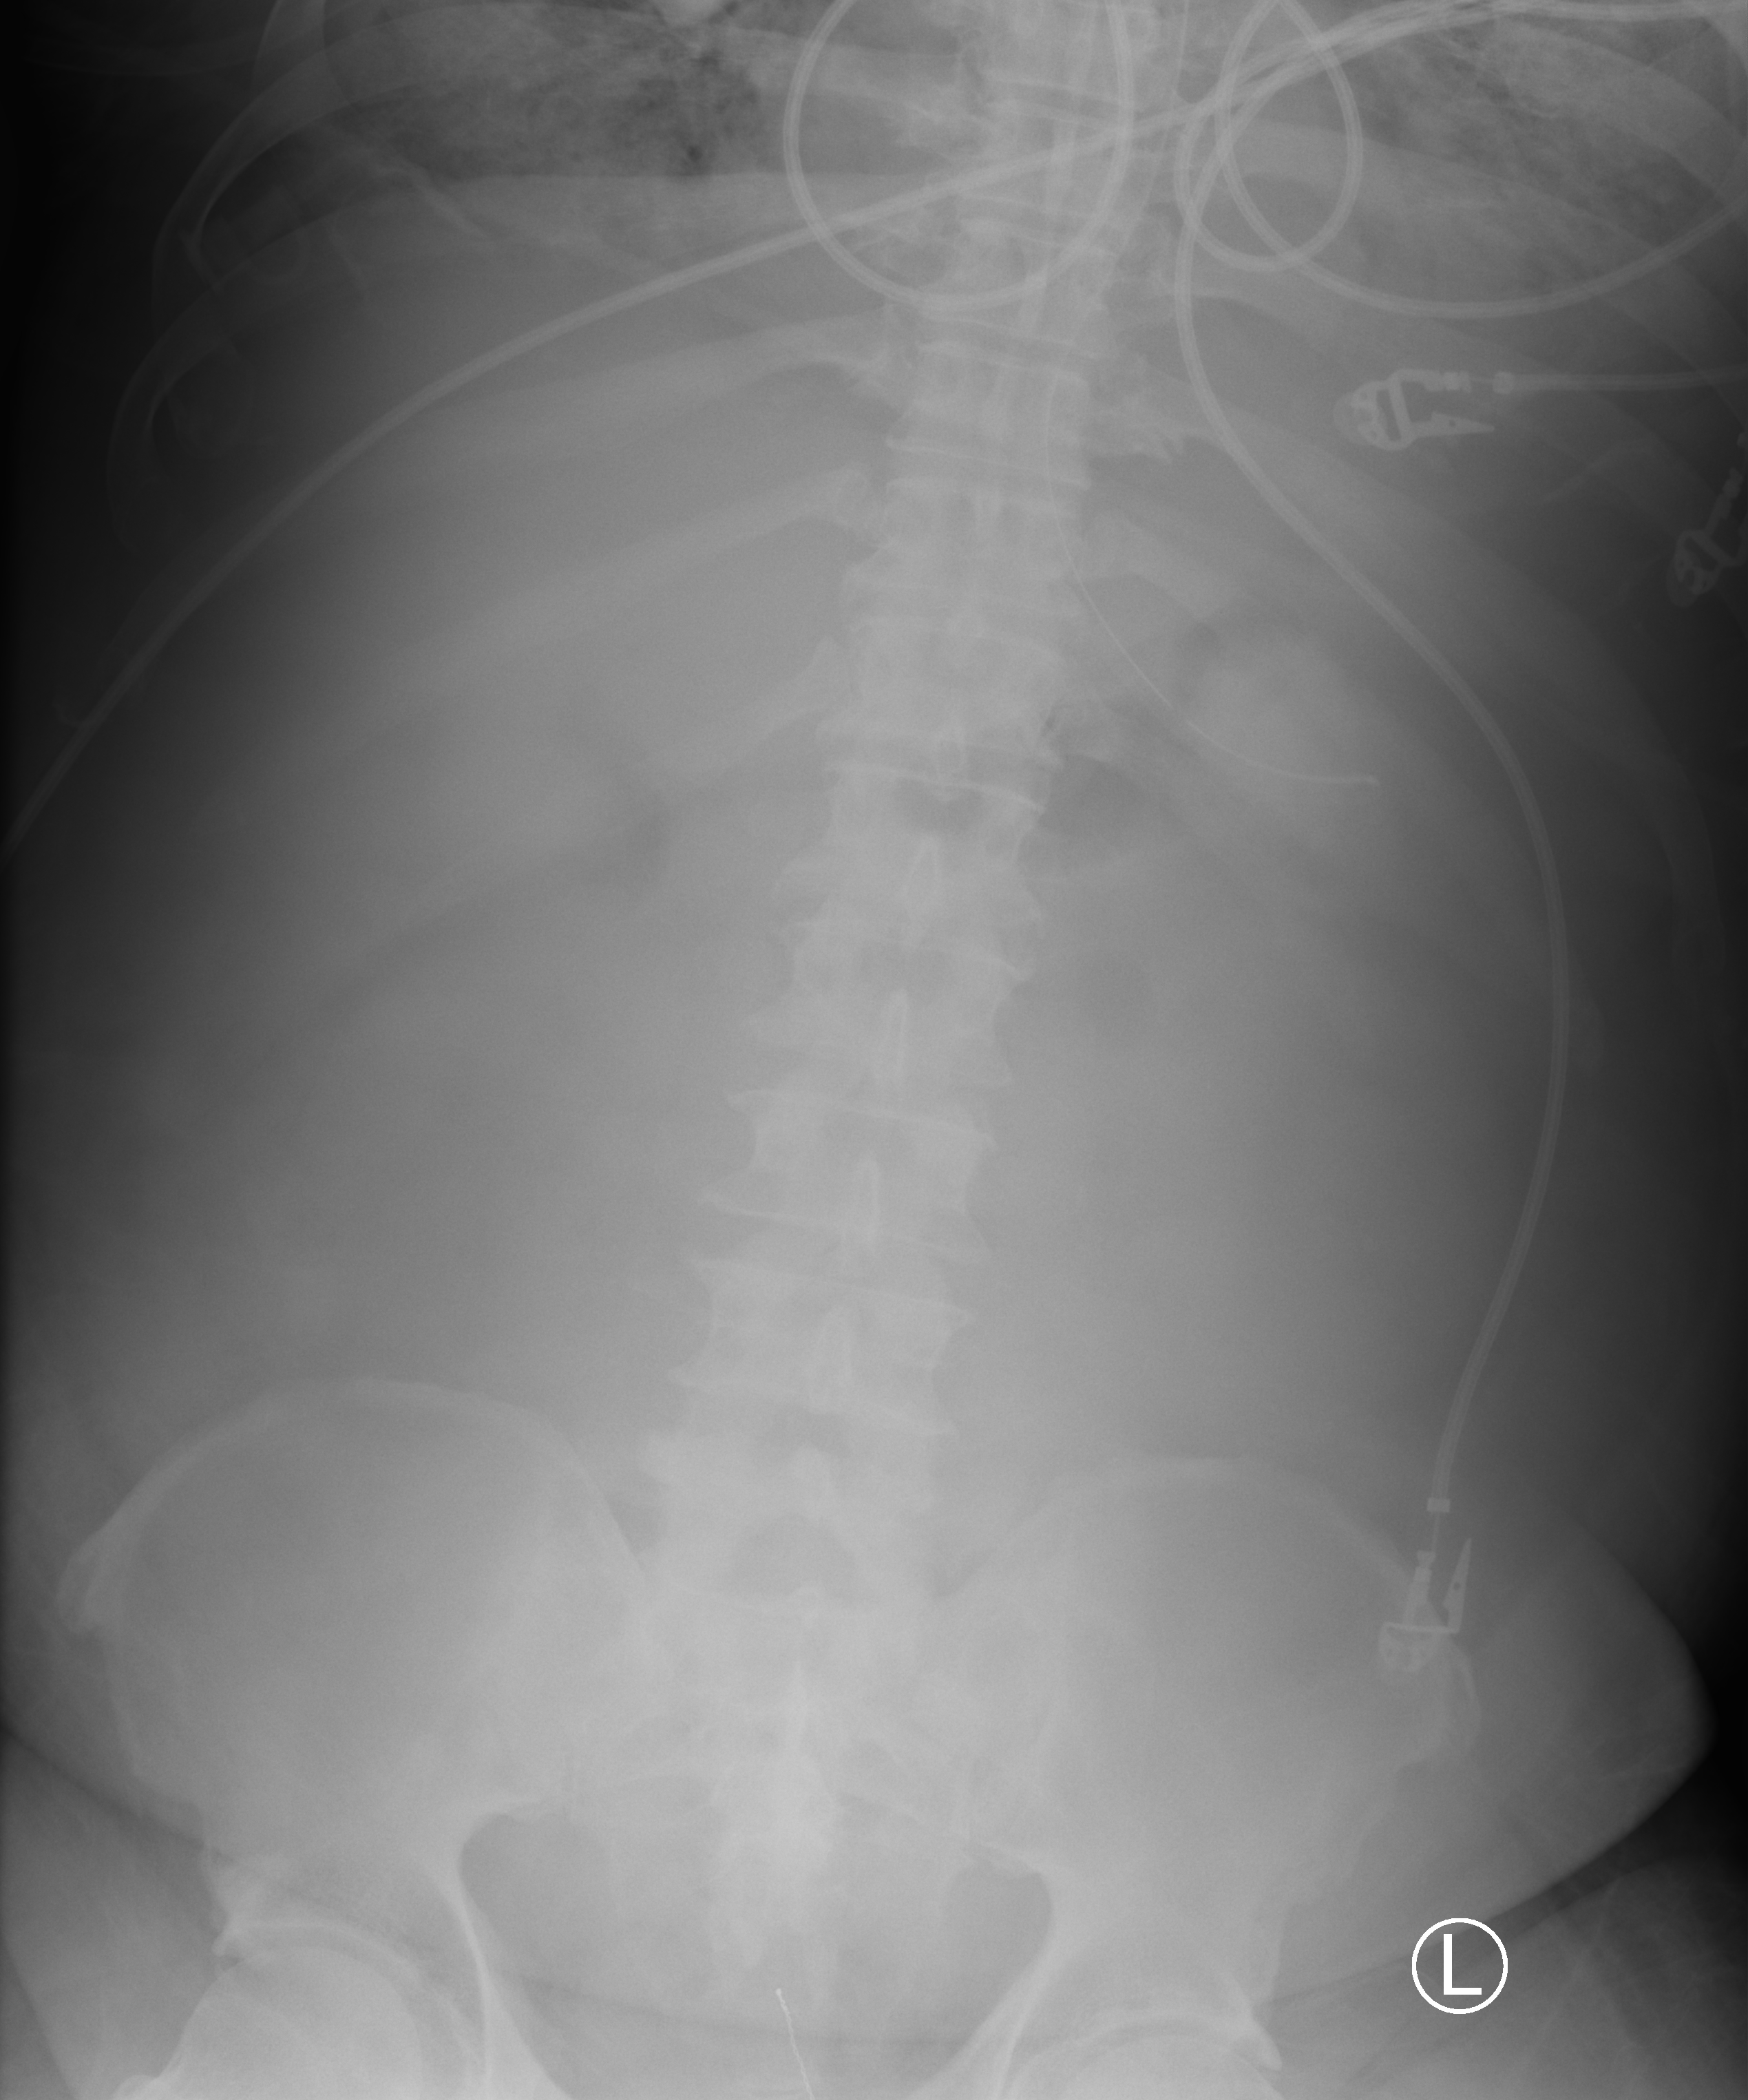
Abdomen X-ray (portable); anteroposterior (AP) projection. Male patient hospitalised with COVID-19, age 60–74 years.
From the hospital-stay record, not from the radiograph (when in the stay this image was taken is not recorded): admitted to intensive care during this hospital stay: yes; length of hospital stay: 28 days; smoking status (admission record): never.